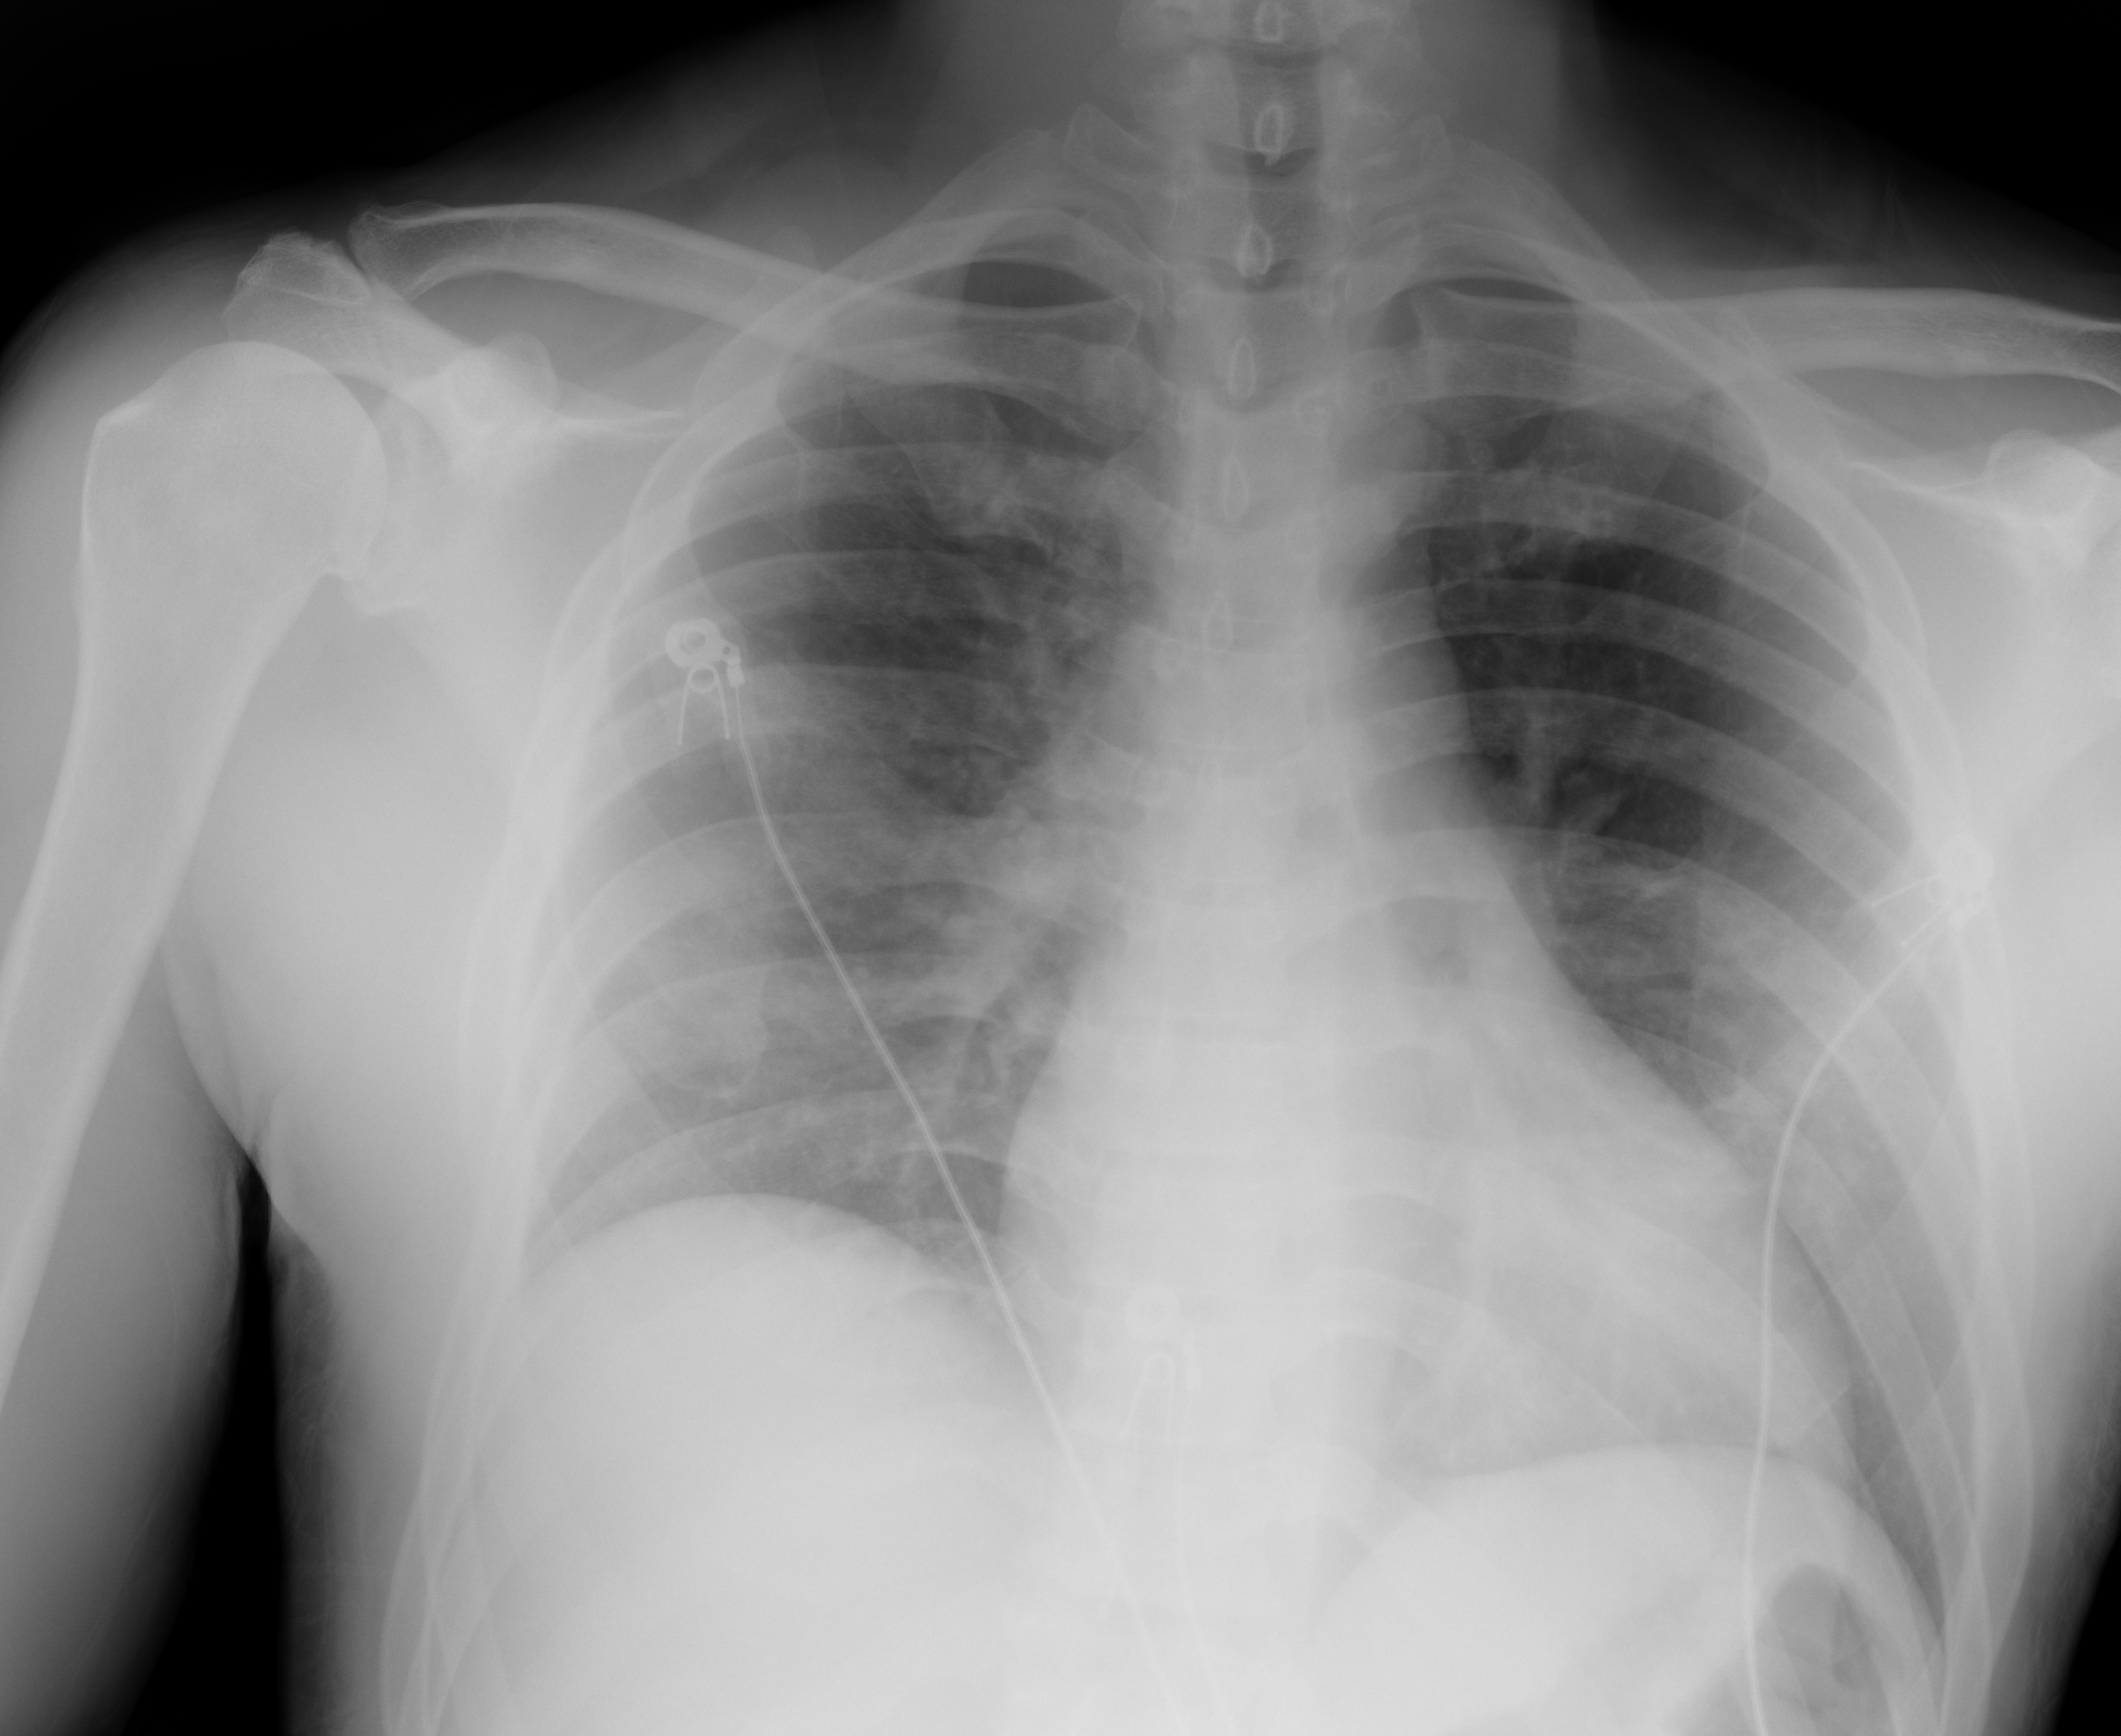
Portable chest radiograph, AP projection. Male patient, age 49 years; COVID-19 (test-positive).
Key findings recorded by the radiologist: Faint airspace opacities in the left mid lung along the left heart border.